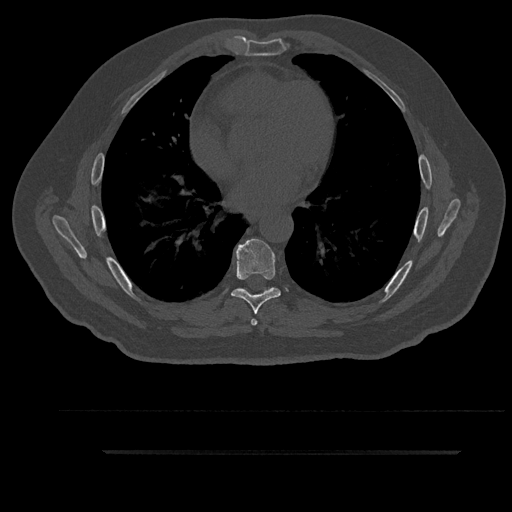
CT including the spine, one axial slice; position 523 of 797 along the scan axis; bone window (W 1800 / L 400 HU); 512 × 512 image matrix, field of view 432 × 432 mm. Patient: male, 63 years. From the clinical record (not read from this slice): primary cancer: renal; vertebrae with lytic lesions (as recorded): T8.
Outlined on this slice (semi-automatic segmentation, software-assisted and operator-edited):
- T6 vertebra: bounding box (x1, y1, x2, y2) in pixels: (241, 288, 270, 326)
- T7 vertebra: (231, 239, 281, 314)
- T8 vertebra: (242, 287, 271, 291)